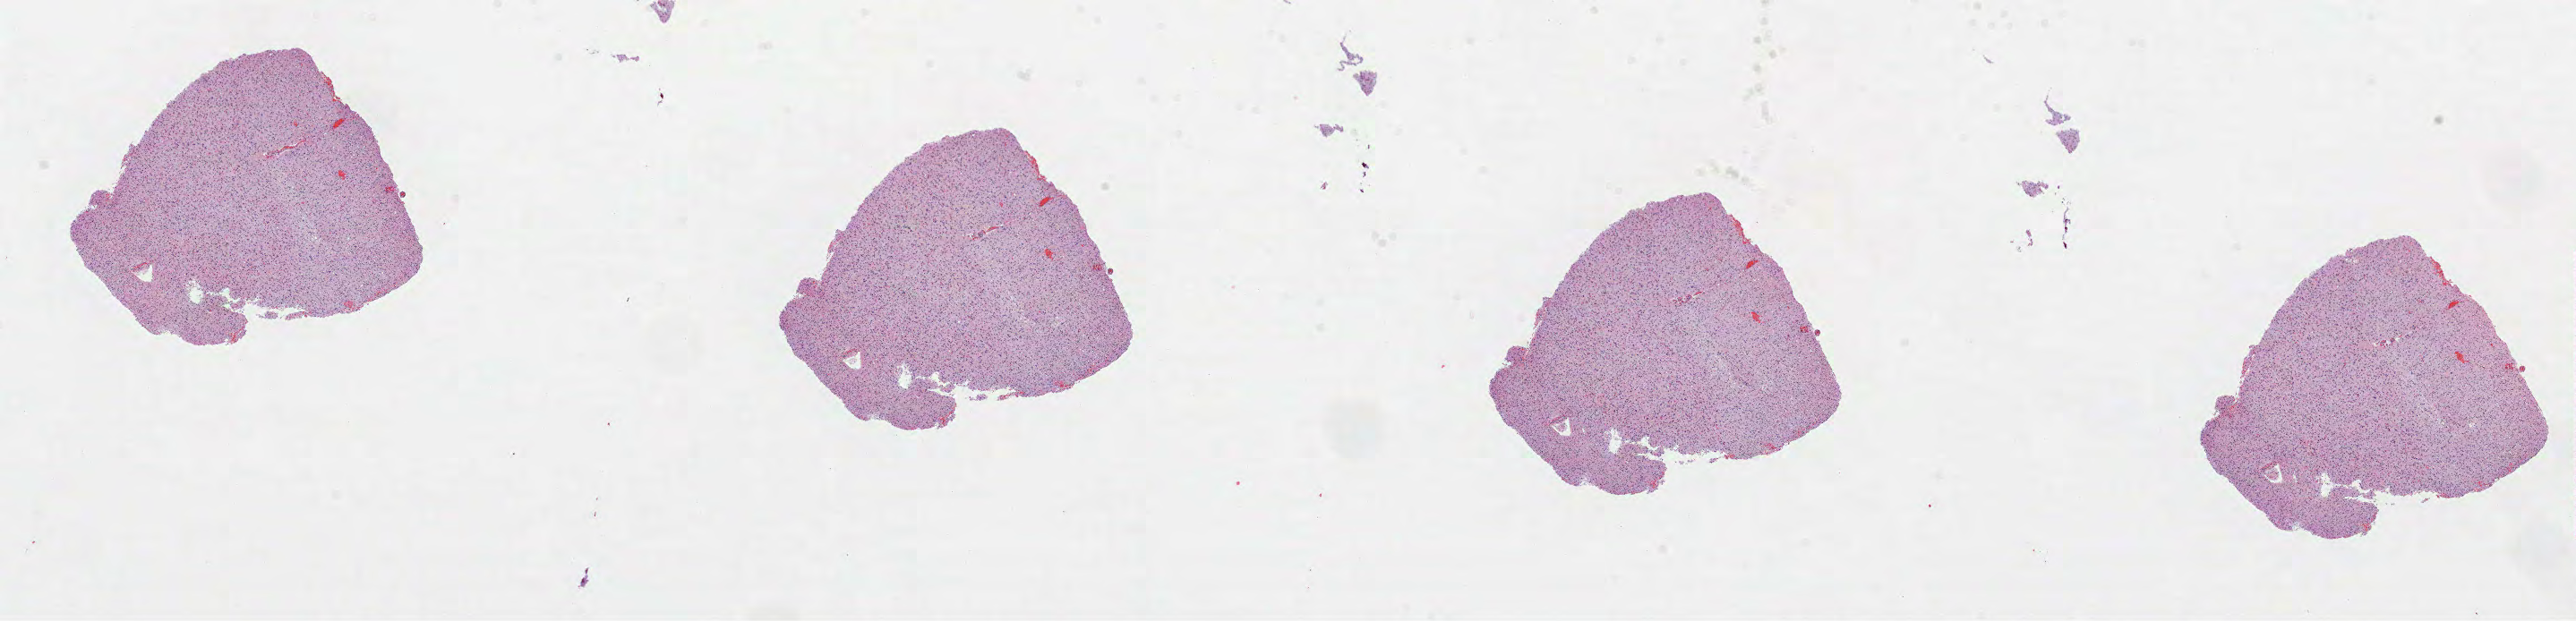
Whole-slide histology image, H&E-stained, whole scanned area (about 23.2 x 5.6 mm, acquisition: 40x scan) shown as a low-resolution overview. Formalin-fixed paraffin-embedded (FFPE) diagnostic section. Sample: primary tumour, brain. Male, age 29 years at initial diagnosis.
Histologic diagnosis: Mixed glioma.